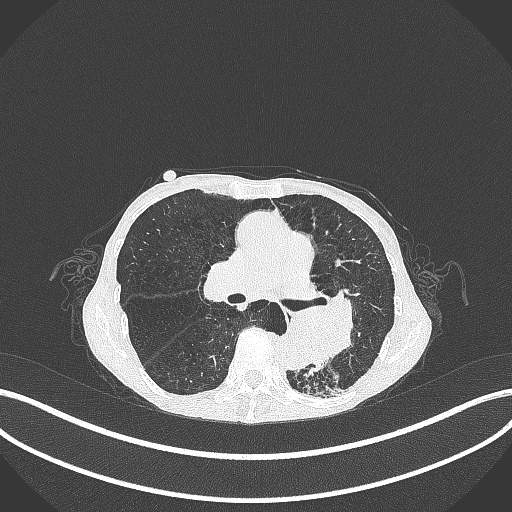
Chest CT, one axial slice. Position 158 of 347 along the scan axis. Reconstruction kernel B70f. 120 kVp. Lung window (W 1500 / L -600 HU). 1 mm slice thickness. 512 × 512 image matrix, field of view 400 × 400 mm. Patient: female, 70 years. From the clinical record (not read from this slice): clinical TNM (as recorded): T3 N0 M0; histopathological grade: G3.
Structures marked on this image (rectangle marked by the reading radiologist):
- lung tumour (recorded histology: small cell carcinoma): box from (x=273, y=292) to (x=357, y=366) px